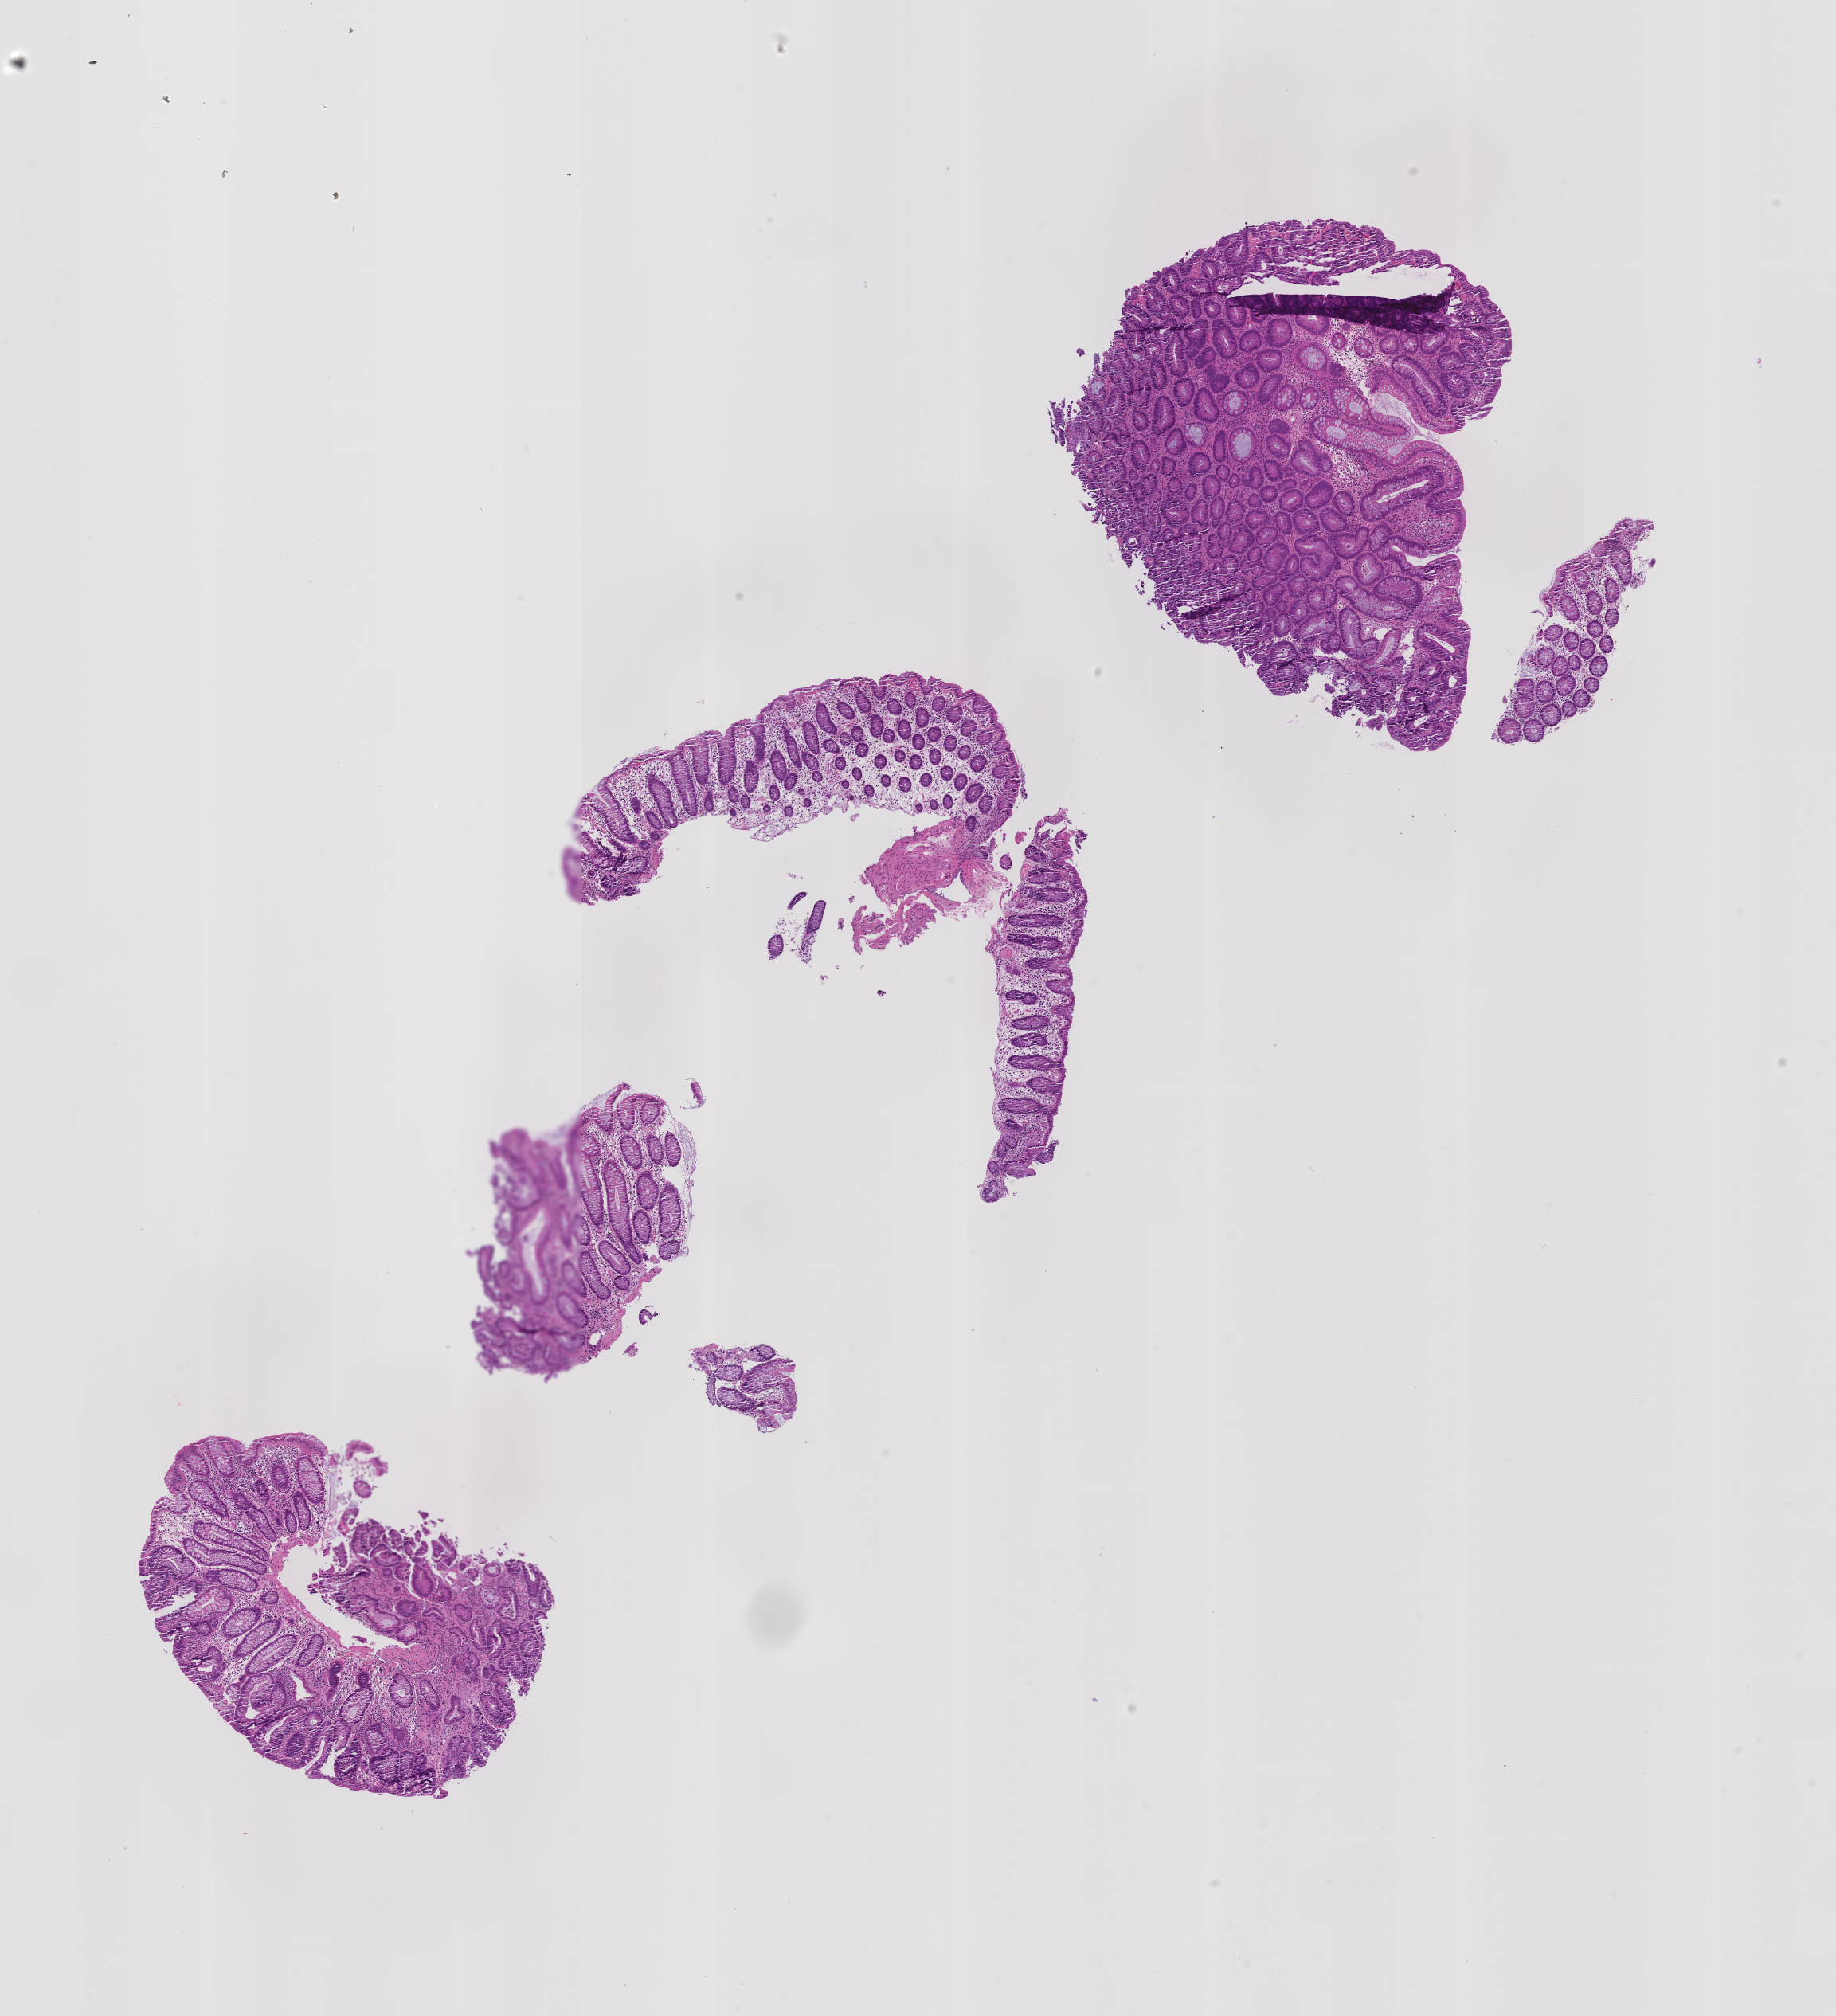
Whole-slide image, hematoxylin and eosin (H&E) stain: colon biopsy, whole scanned area (about 9.2 x 10.1 mm) shown as a low-resolution overview, formalin-fixed paraffin-embedded section, site: ascending colon. Patient: male.
- lesion category (as recorded): premalignant